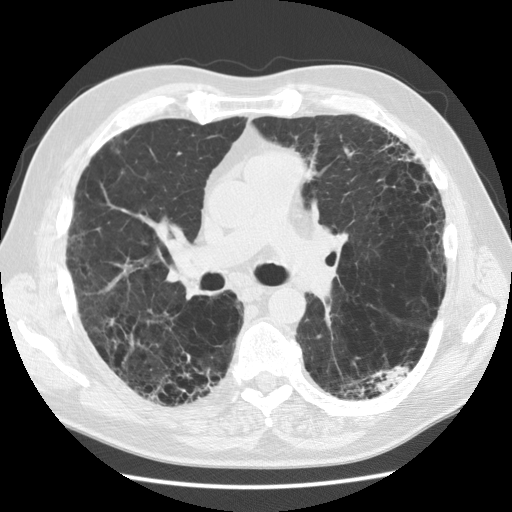
Low-dose screening chest CT, one axial slice. Position 72 of 128 along the scan axis. 120 kVp. Lung window (W 1500 / L -600 HU). 2.5 mm slice thickness. 512 × 512 image matrix, field of view 360 × 360 mm.
Annotated regions visible in this slice (outlined manually by an expert reader):
- lesion 1 (tumor, lower lobe of left lung): bounding box <368,363,410,393> (left, top, right, bottom; pixels)